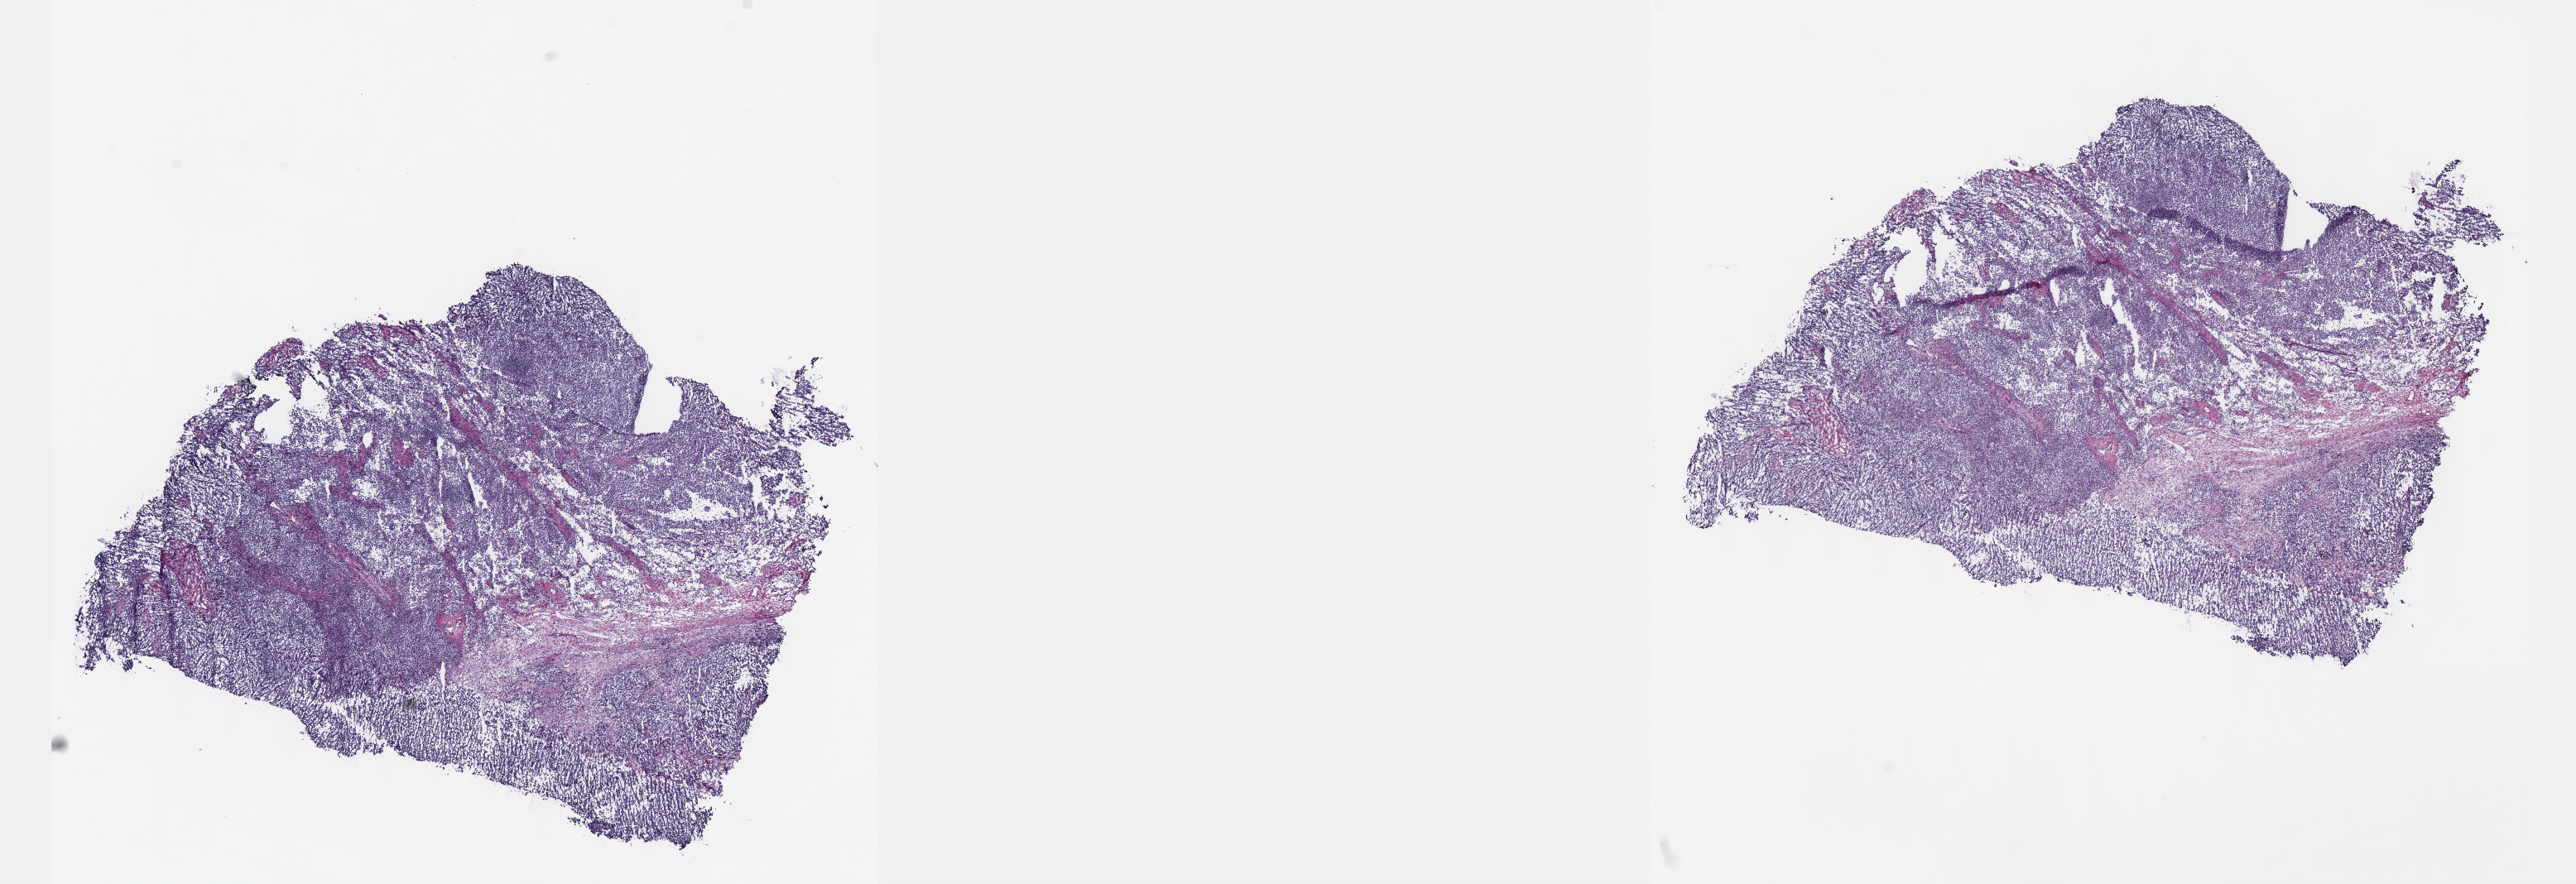
Whole-slide histology image, Hematoxylin and eosin (H&E) stained — shown as a low-resolution overview of the whole scanned area (about 25.1 x 8.6 mm, slide scanned at 40x). Frozen section from the top of the tissue portion. Additional new primary tumour sample from the testis. Patient: male, age at initial diagnosis 22 years. Composition of this section per pathologist review: tumour cells 80%, tumour nuclei 70%, normal cells 0%, stromal cells 20%, necrosis 0%. Inflammatory infiltration, as recorded: lymphocyte infiltration 90%, monocyte infiltration 10%, neutrophil infiltration 0%.
This section: additional new primary tumour. Patient diagnosis: Embryonal carcinoma, NOS.